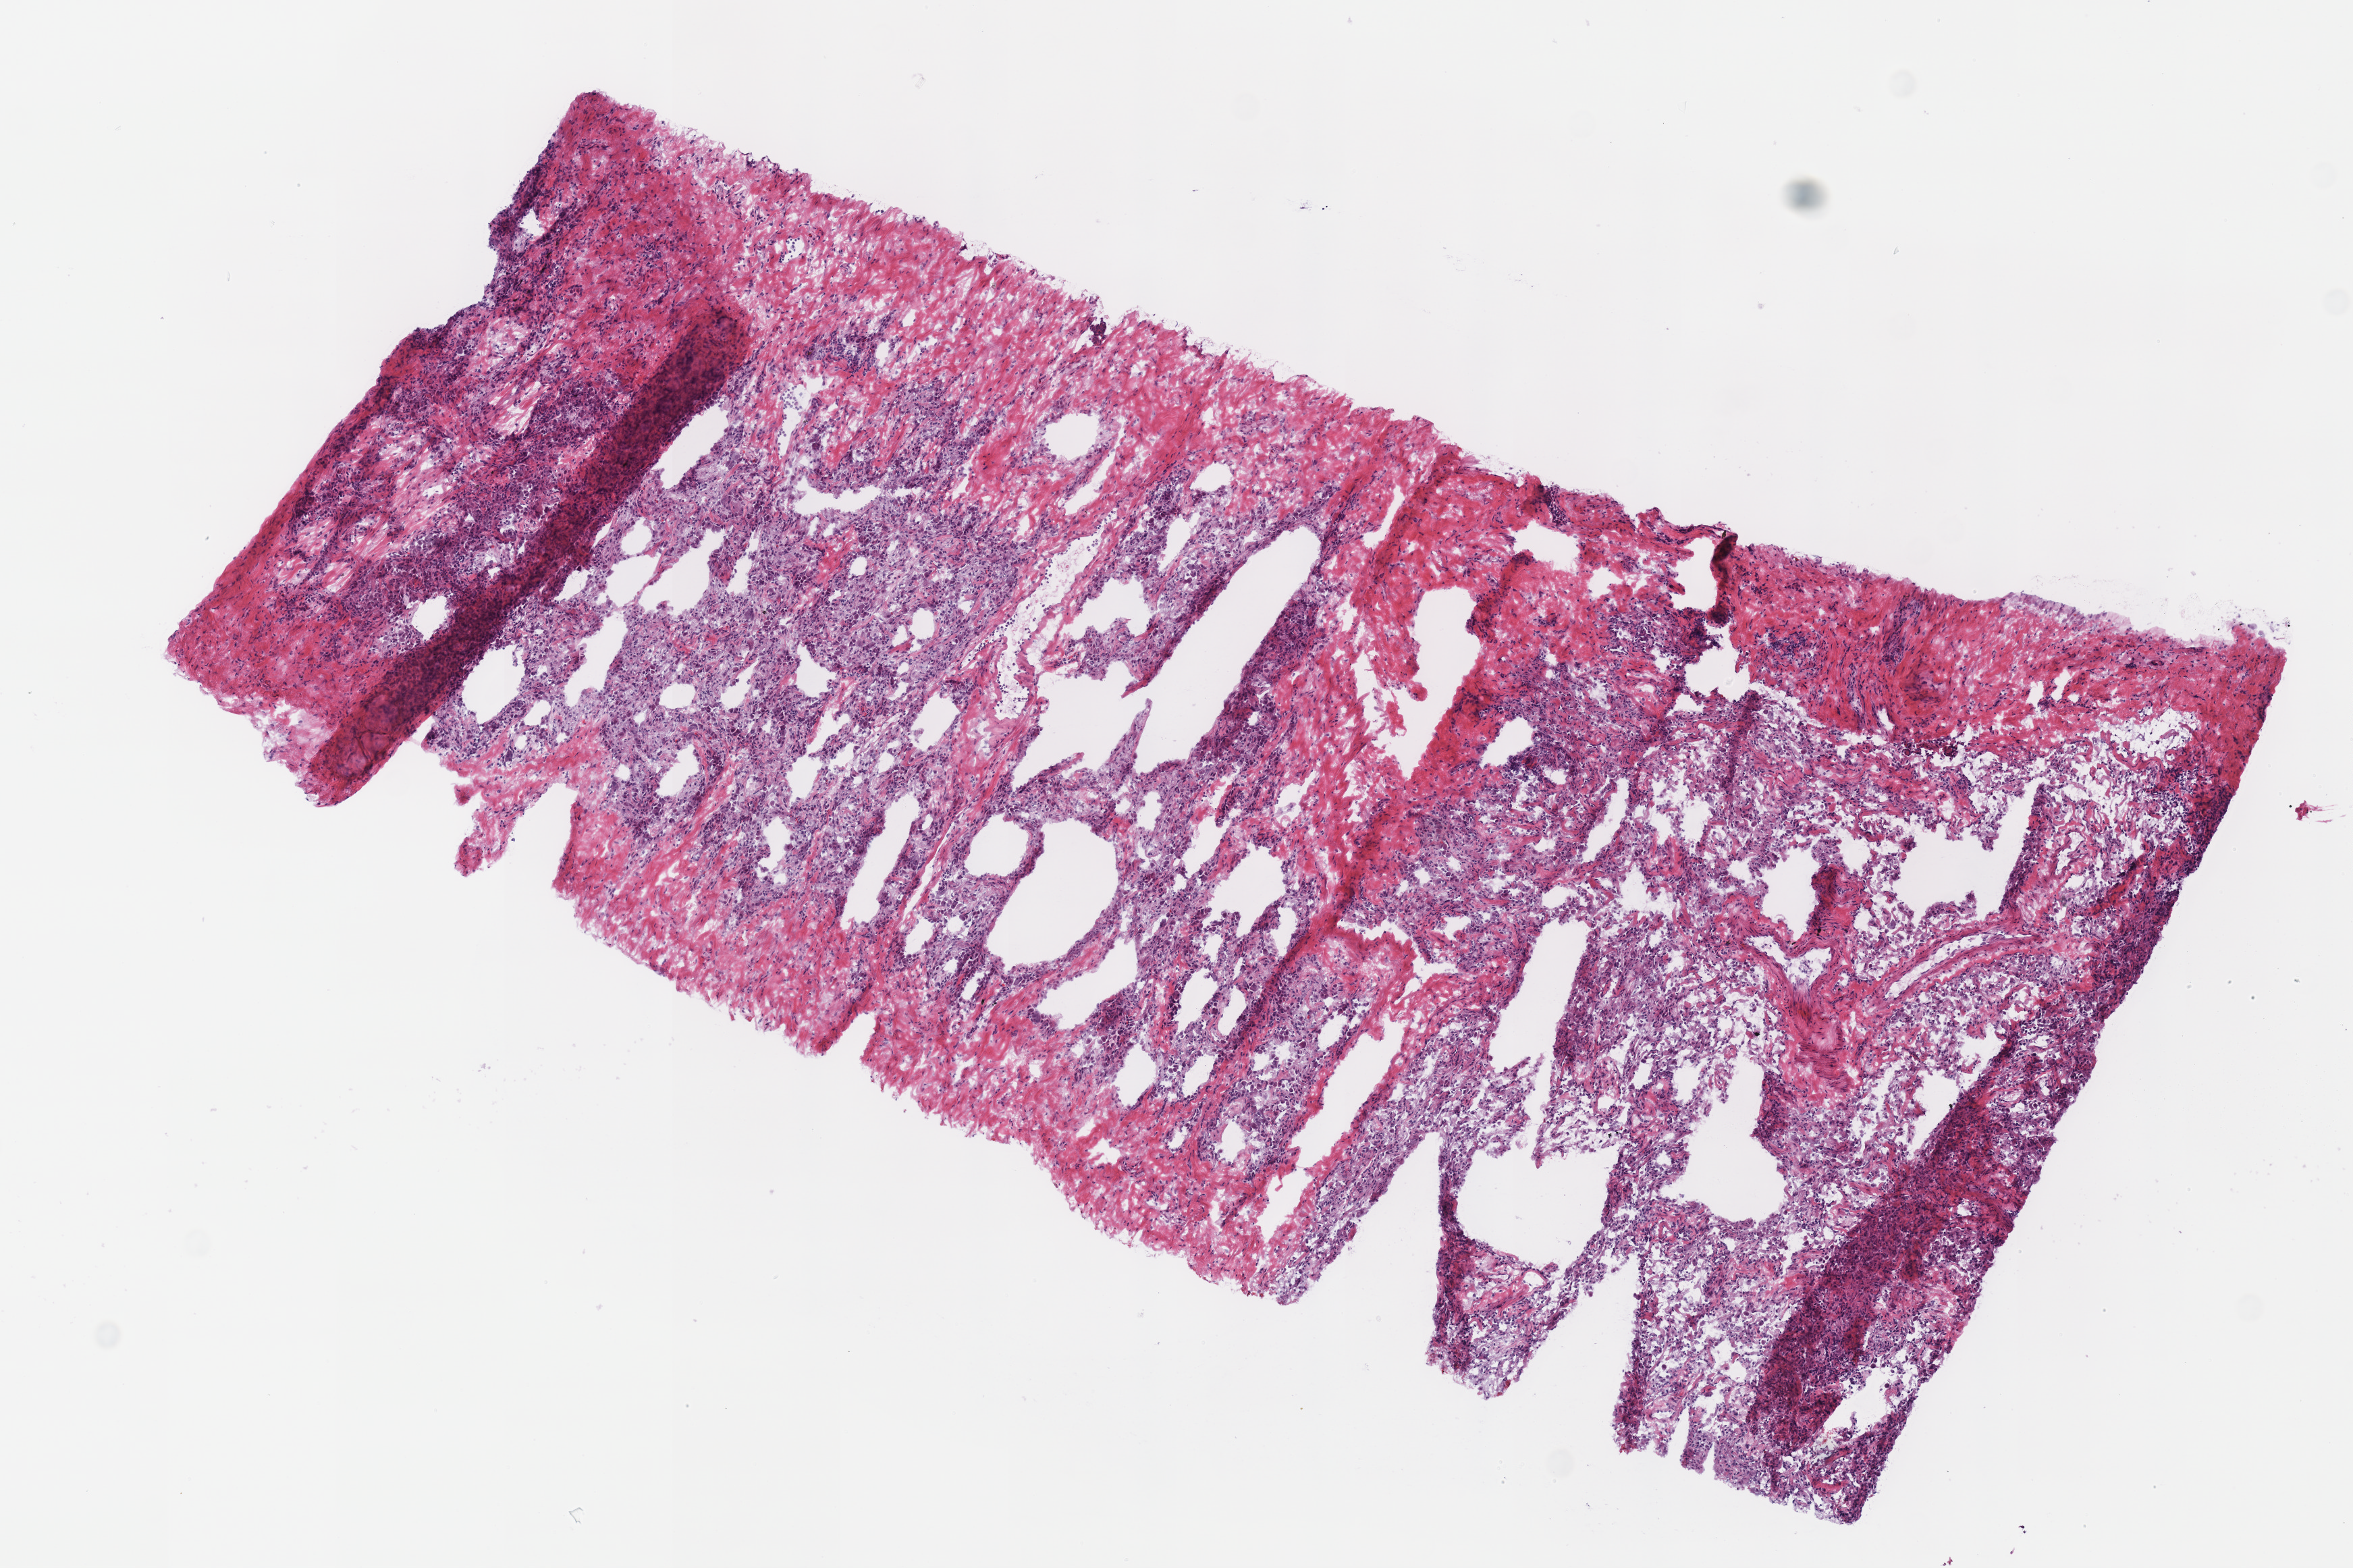
H&E-stained whole-slide image, shown as a low-resolution overview of the whole scanned area (about 6.9 x 4.6 mm, slide scanned at 40x), frozen section, solid tissue normal (non-tumour tissue) sample from the lung. Male patient; age at initial diagnosis 60 years.
This section: solid tissue normal sample (biorepository sample class). Patient diagnosis: Adenocarcinoma, NOS (upper lobe, lung).